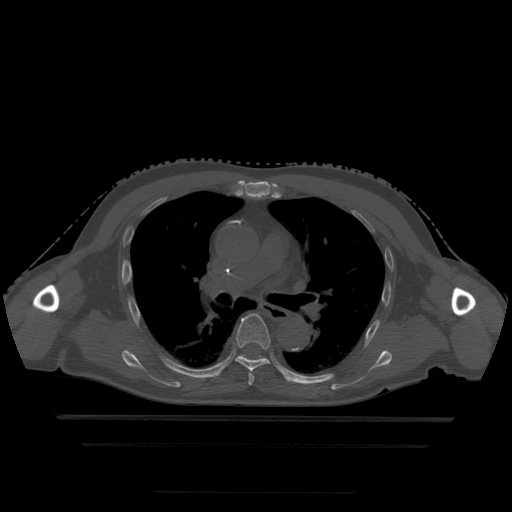
CT including the spine, one axial slice; position 317 of 522 along the scan axis; bone window (W 1800 / L 400 HU); 512 × 512 image matrix, field of view 436 × 436 mm. Patient age 68 years. Case-level facts recorded for this patient, not image findings: primary cancer: urothelial.
Outlined on this slice (semi-automatically segmented with operator editing):
- T5 vertebra: bounding box [x1, y1, x2, y2] px = [248, 374, 255, 386]
- T6 vertebra: [235, 314, 271, 372]
- T7 vertebra: [241, 355, 266, 359]